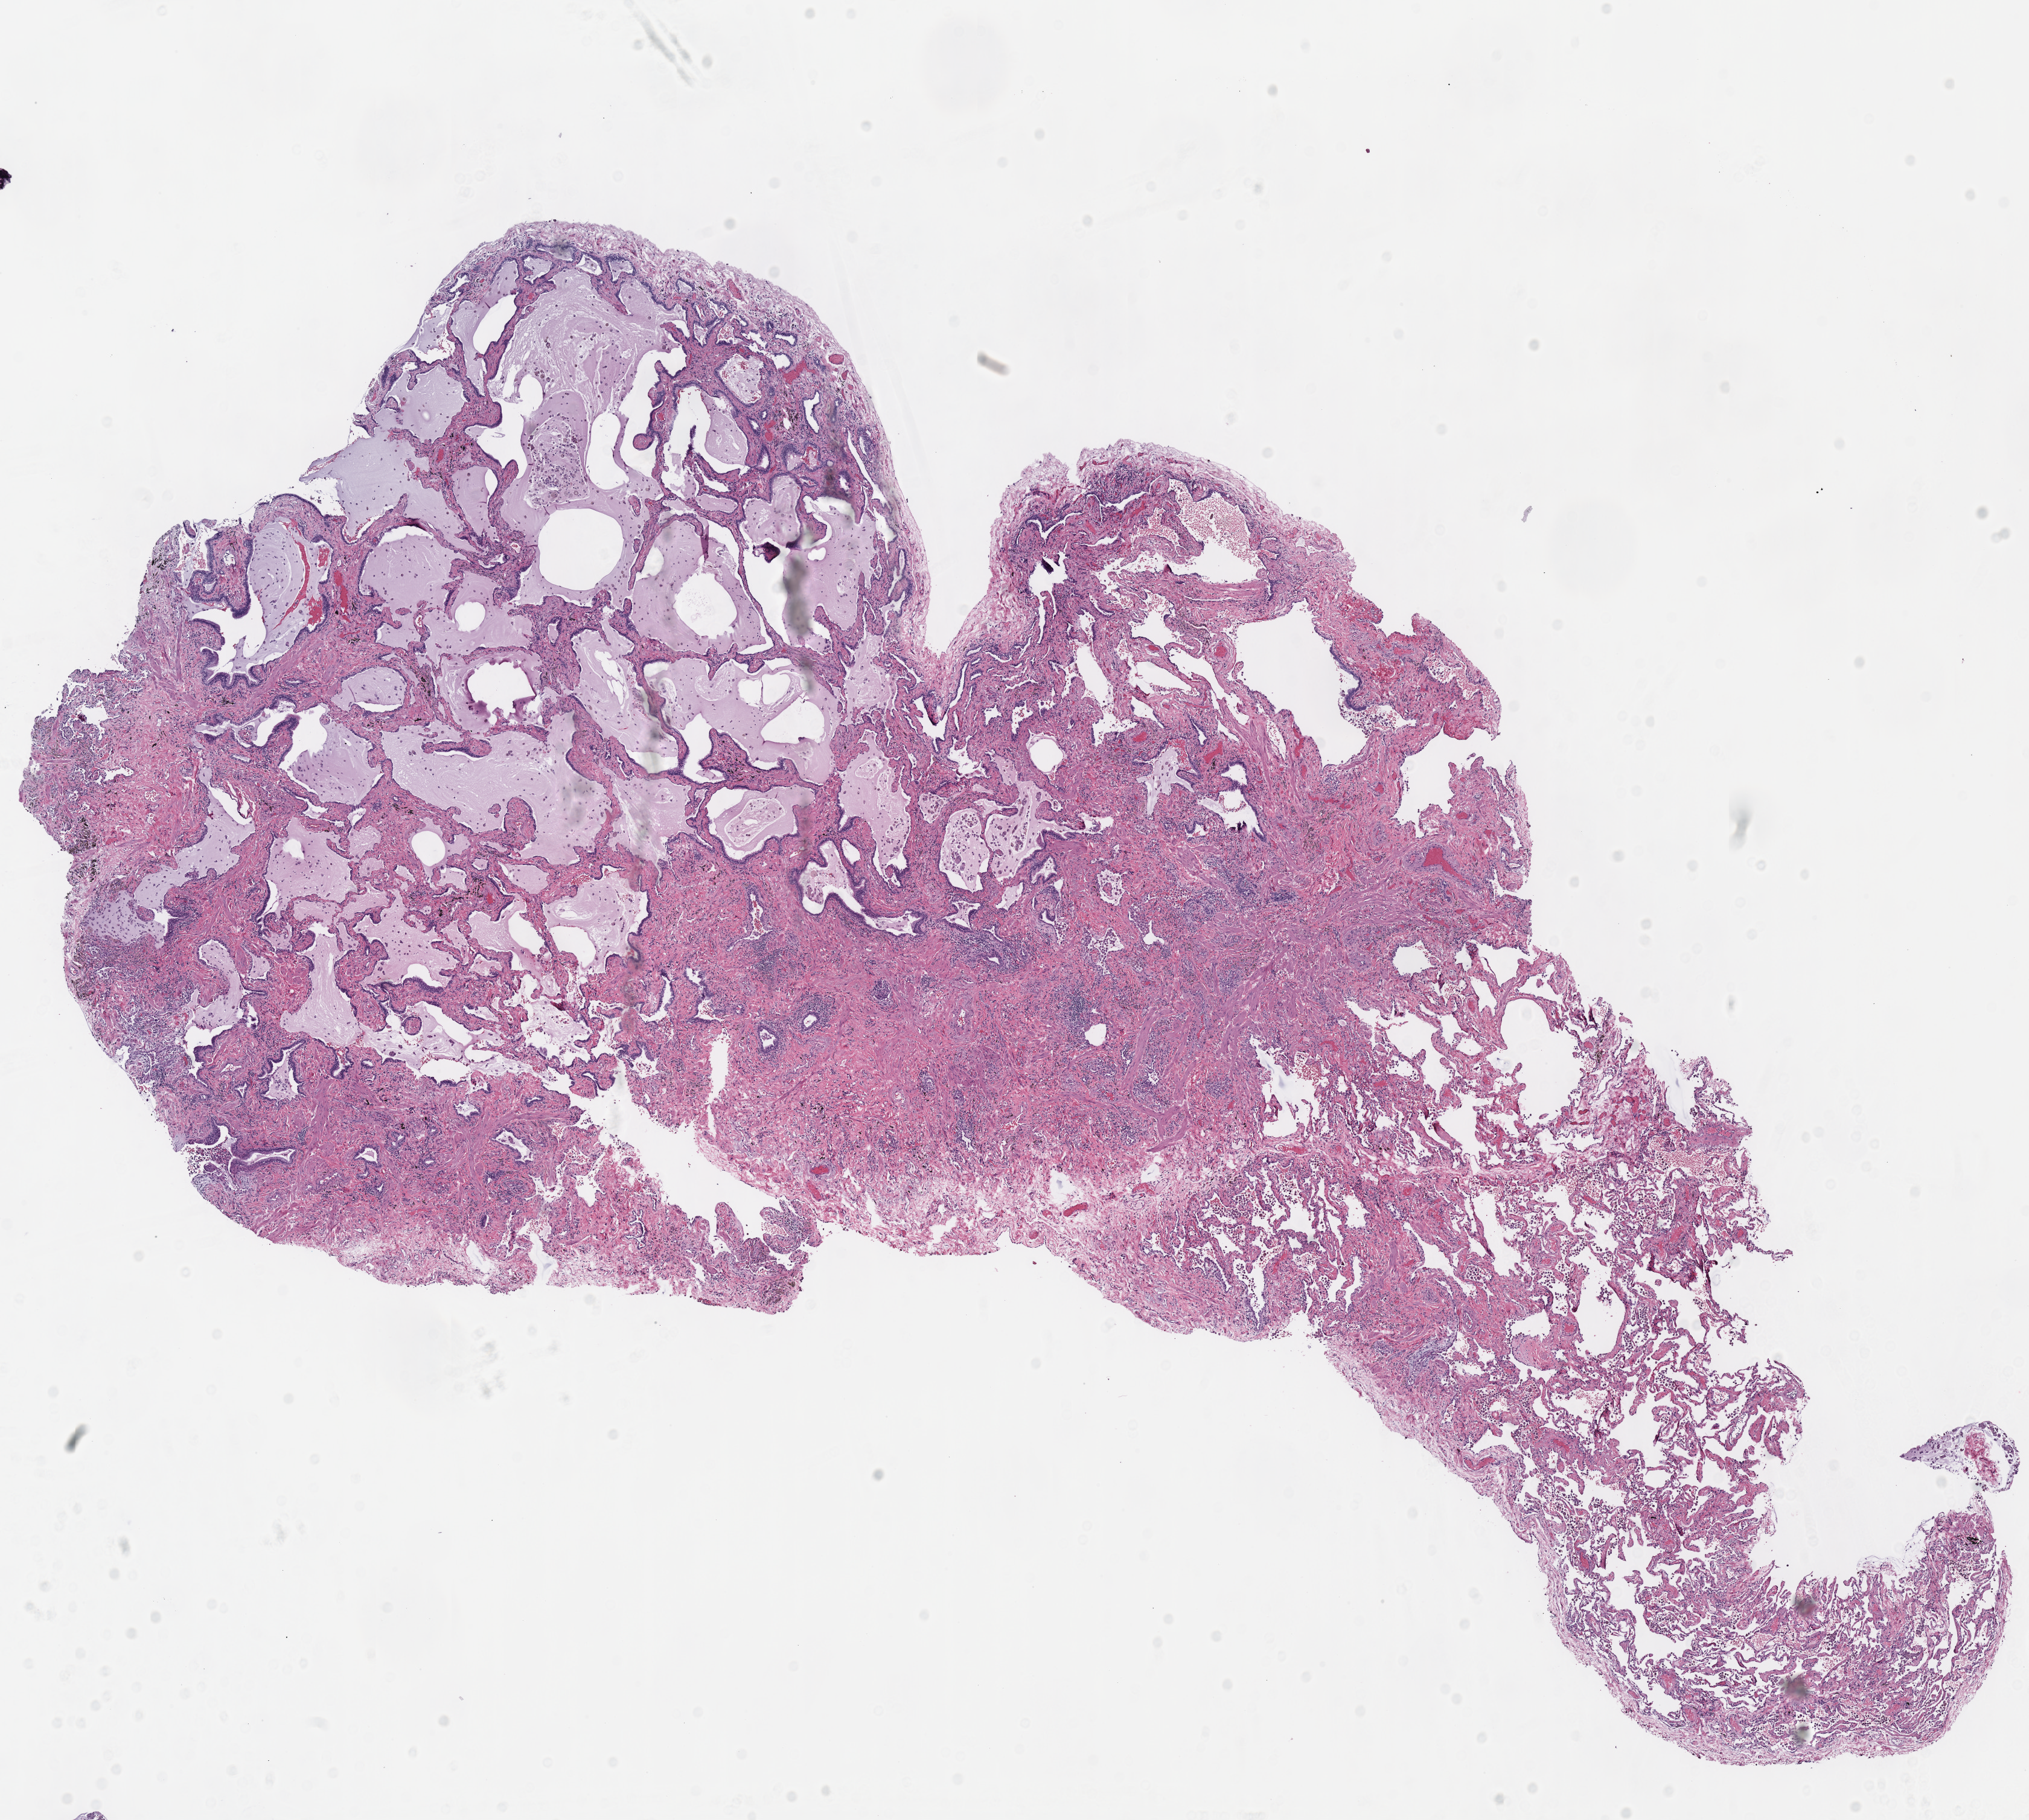
Digitized Hematoxylin and eosin (H&E) stained tissue section (whole slide) — whole scanned area (about 13.2 x 11.9 mm) shown as a low-resolution overview. Frozen section from the top of the tissue portion. Lung, solid tissue normal (non-tumour tissue) sample. Male patient; age at initial diagnosis 72 years.
This section: solid tissue normal (non-tumour) sample from the same patient. Patient diagnosis: Adenocarcinoma, NOS (upper lobe, lung).